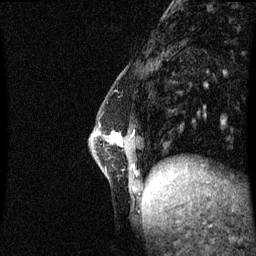
Breast MRI (dynamic contrast-enhanced), one sagittal slice; slice 19 of 60 in the series (ordered by position); dynamic contrast-enhanced series, image 2 of 3 at this slice position (ordered by acquisition); 1.5 T; TE 4.2 ms, TR 8.9 ms; 2.2 mm slice thickness; 256 × 256 image matrix, field of view 210 × 210 mm. Female patient, age 47 years. From the clinical record (not read from this slice): setting: breast cancer imaged before/during neoadjuvant chemotherapy; receptor status: HR-positive, HER2-negative.
Outlined on this slice (semi-automatic segmentation, software-assisted and operator-edited):
- analysis volume of interest (the breast-tissue region the enhancement analysis was run in; not a lesion): bounding box [x1, y1, x2, y2] px = [90, 132, 141, 193]
- tumour enhancement mask (voxels above the 70 % enhancement threshold inside the analysis volume of interest): [111, 133, 122, 145]